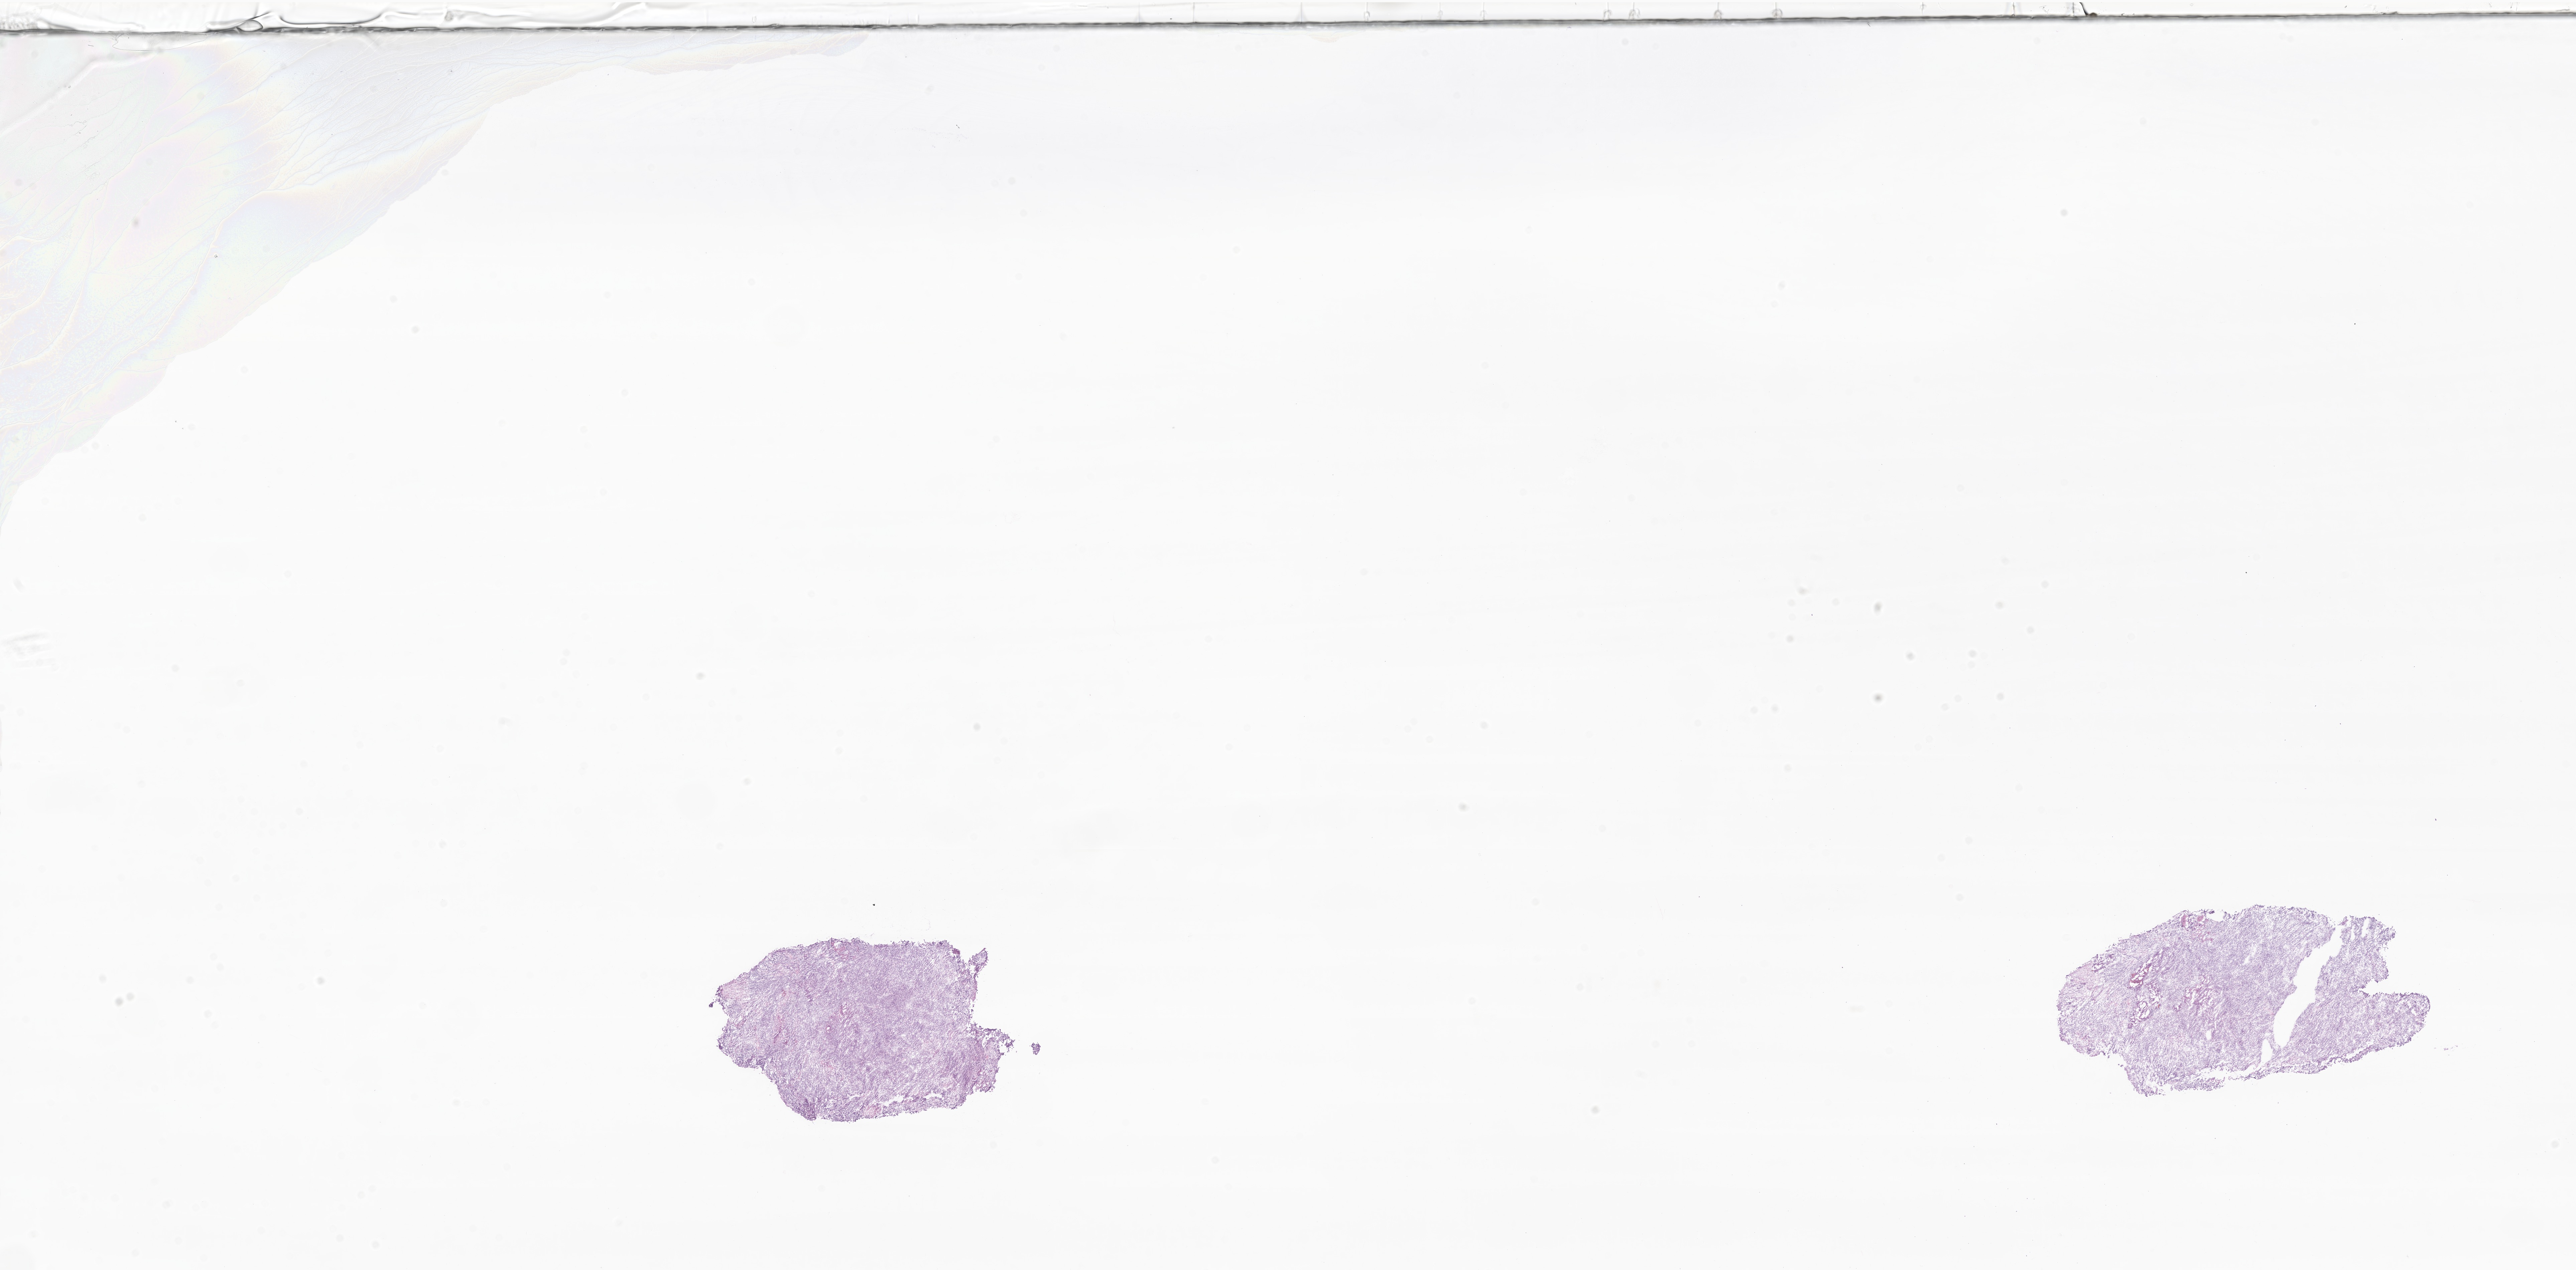
Digitized H&E-stained section of tumor tissue from the brain — whole scanned area (about 32.5 x 16.0 mm) shown as a low-resolution overview. Frozen section. Male patient, age 61 days.
Recorded diagnosis: Neoplasm, uncertain whether benign or malignant.